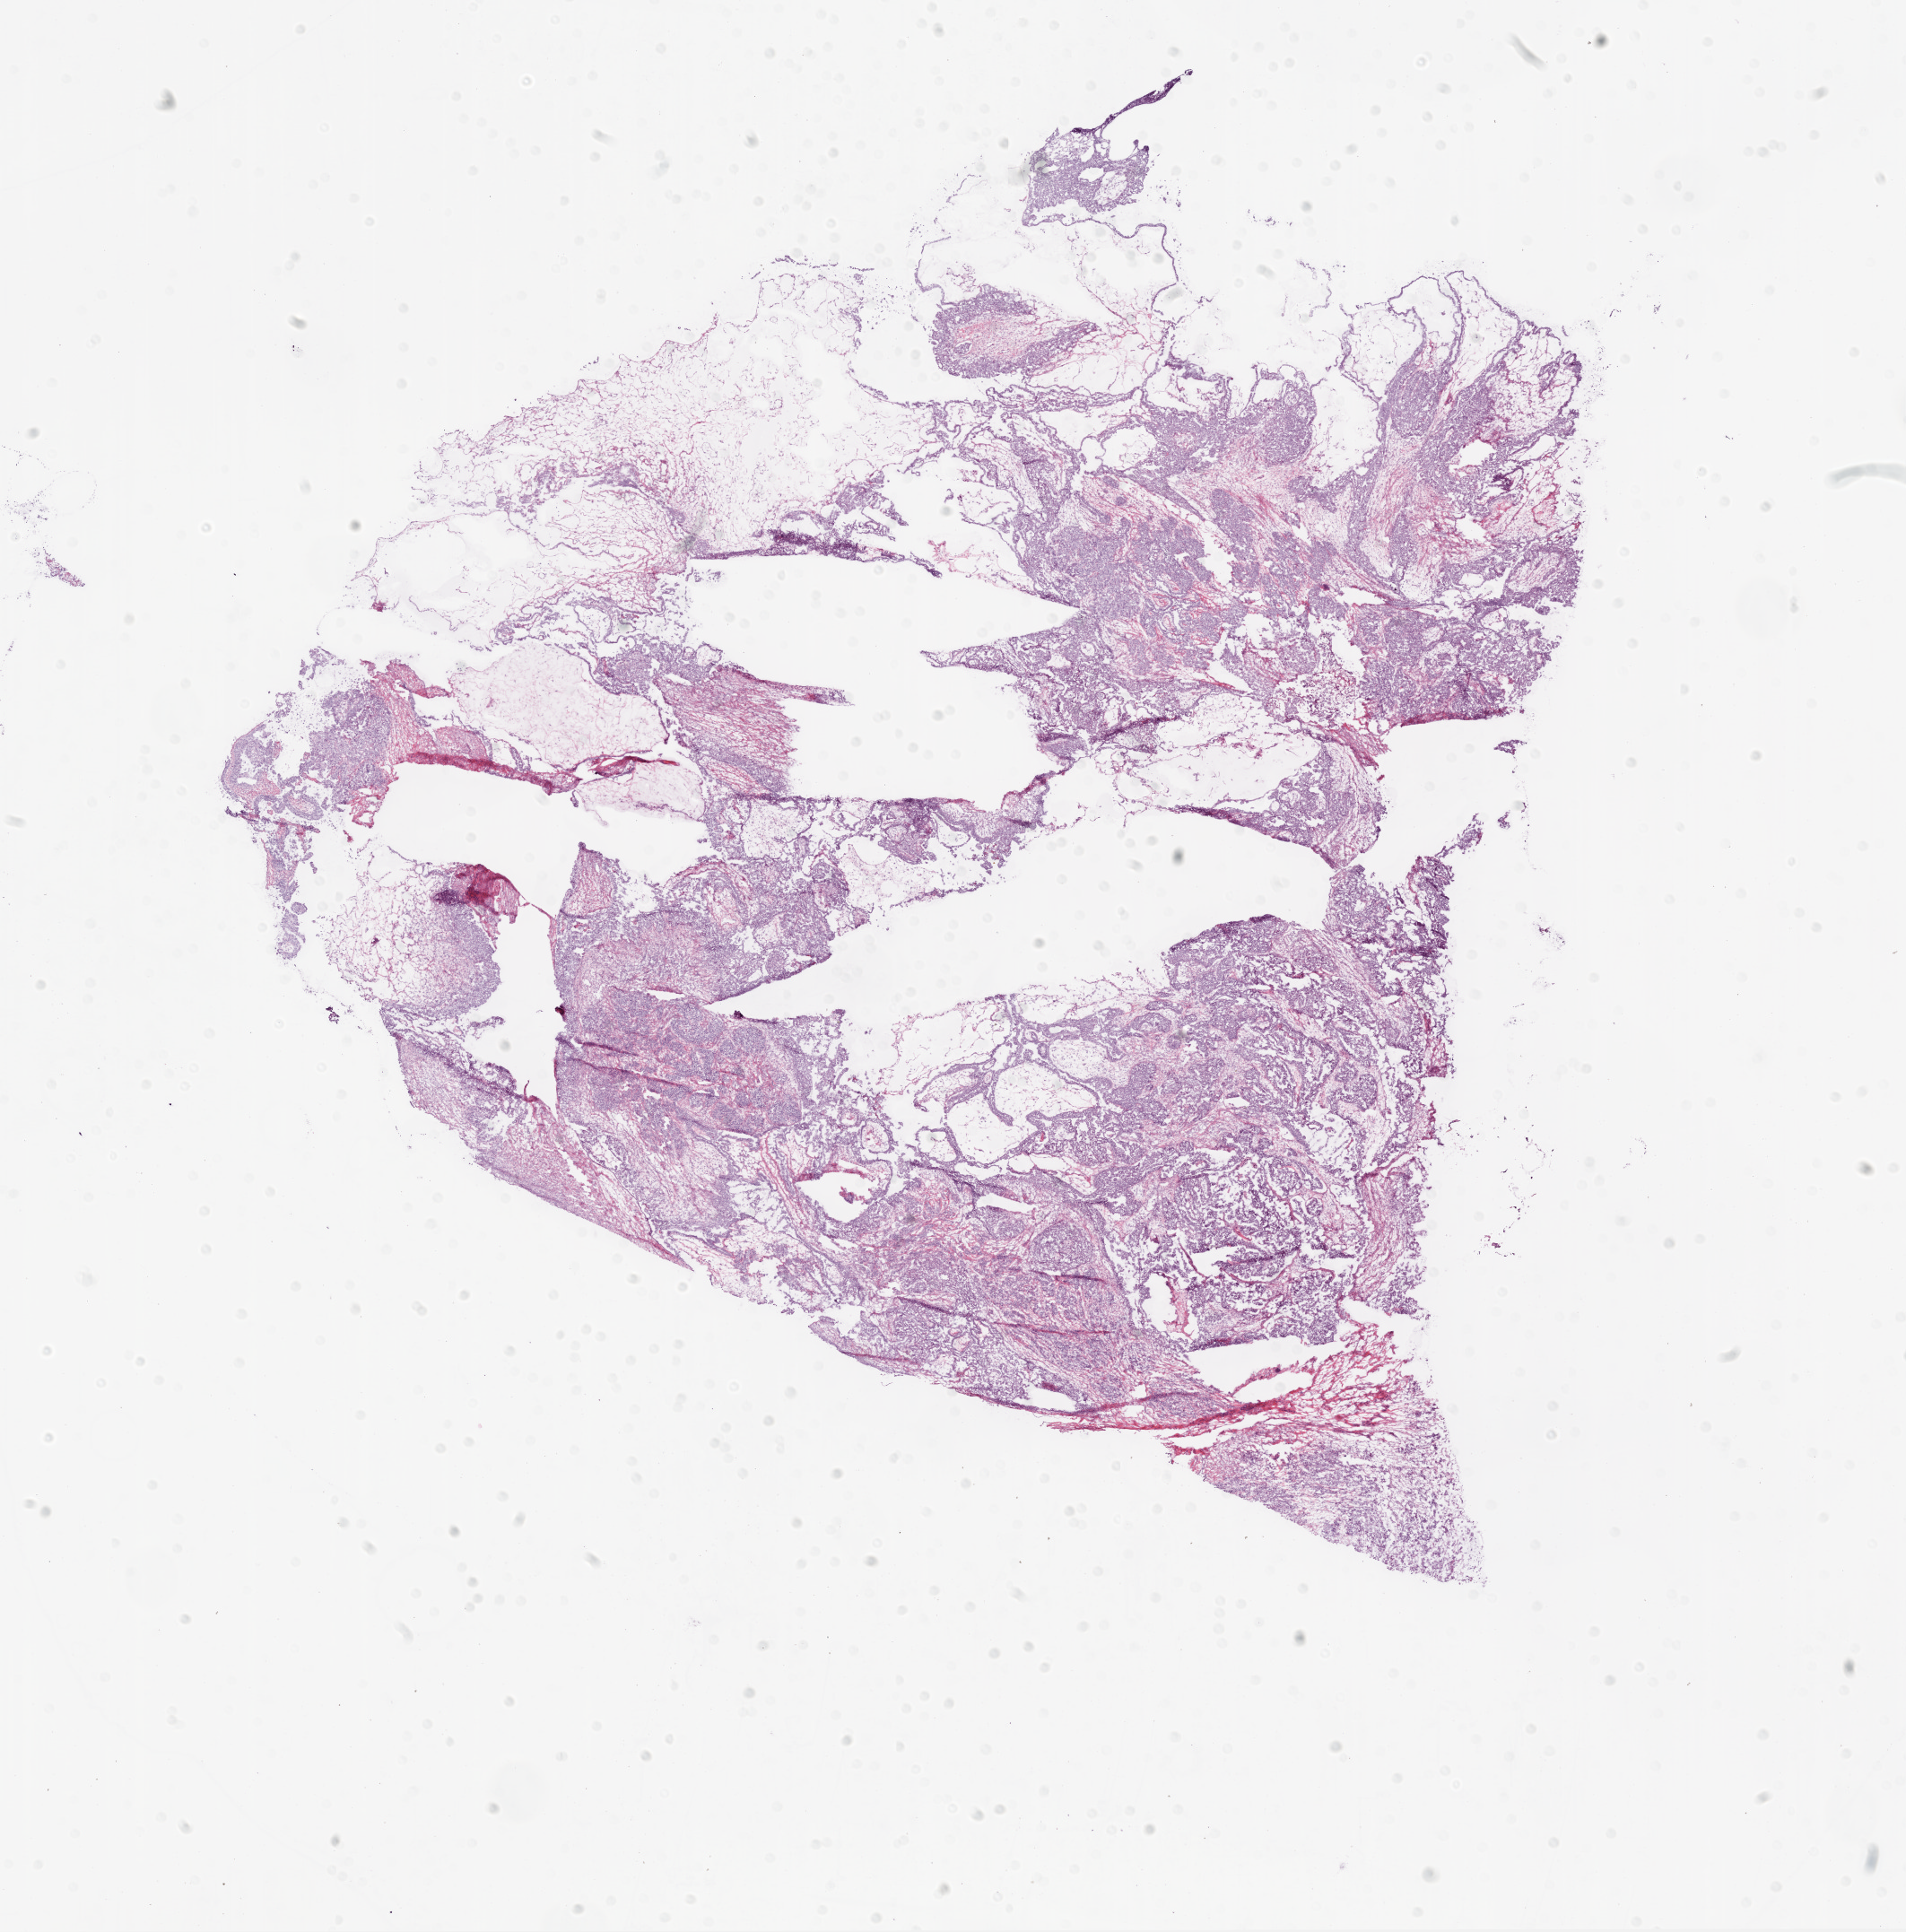
Digitized Hematoxylin and eosin (H&E) stained tissue section (whole slide) — whole scanned area (about 17.1 x 17.3 mm, slide scanned at 20x) shown as a low-resolution overview. Frozen section from the bottom of the tissue portion. Ovary, primary tumour sample. Patient: female, age at initial diagnosis 65 years. Composition of this section per pathologist review: tumour cells 80%, tumour nuclei 80%.
Diagnosis: Serous cystadenocarcinoma, NOS.